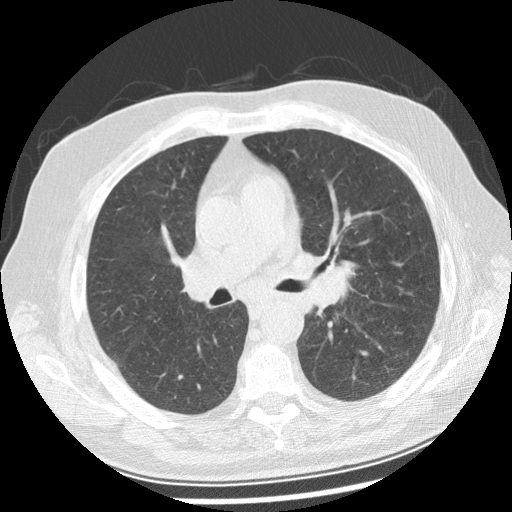
Low-dose screening chest CT, one axial slice. Reconstruction kernel STANDARD. Lung window (W 1500 / L -600 HU). 2.5 mm slice thickness. 512 × 512 image matrix.
Outlined on this slice (manually delineated by an expert):
- lesion 1 (tumor, left main bronchus): box from (x=306, y=260) to (x=356, y=310) px